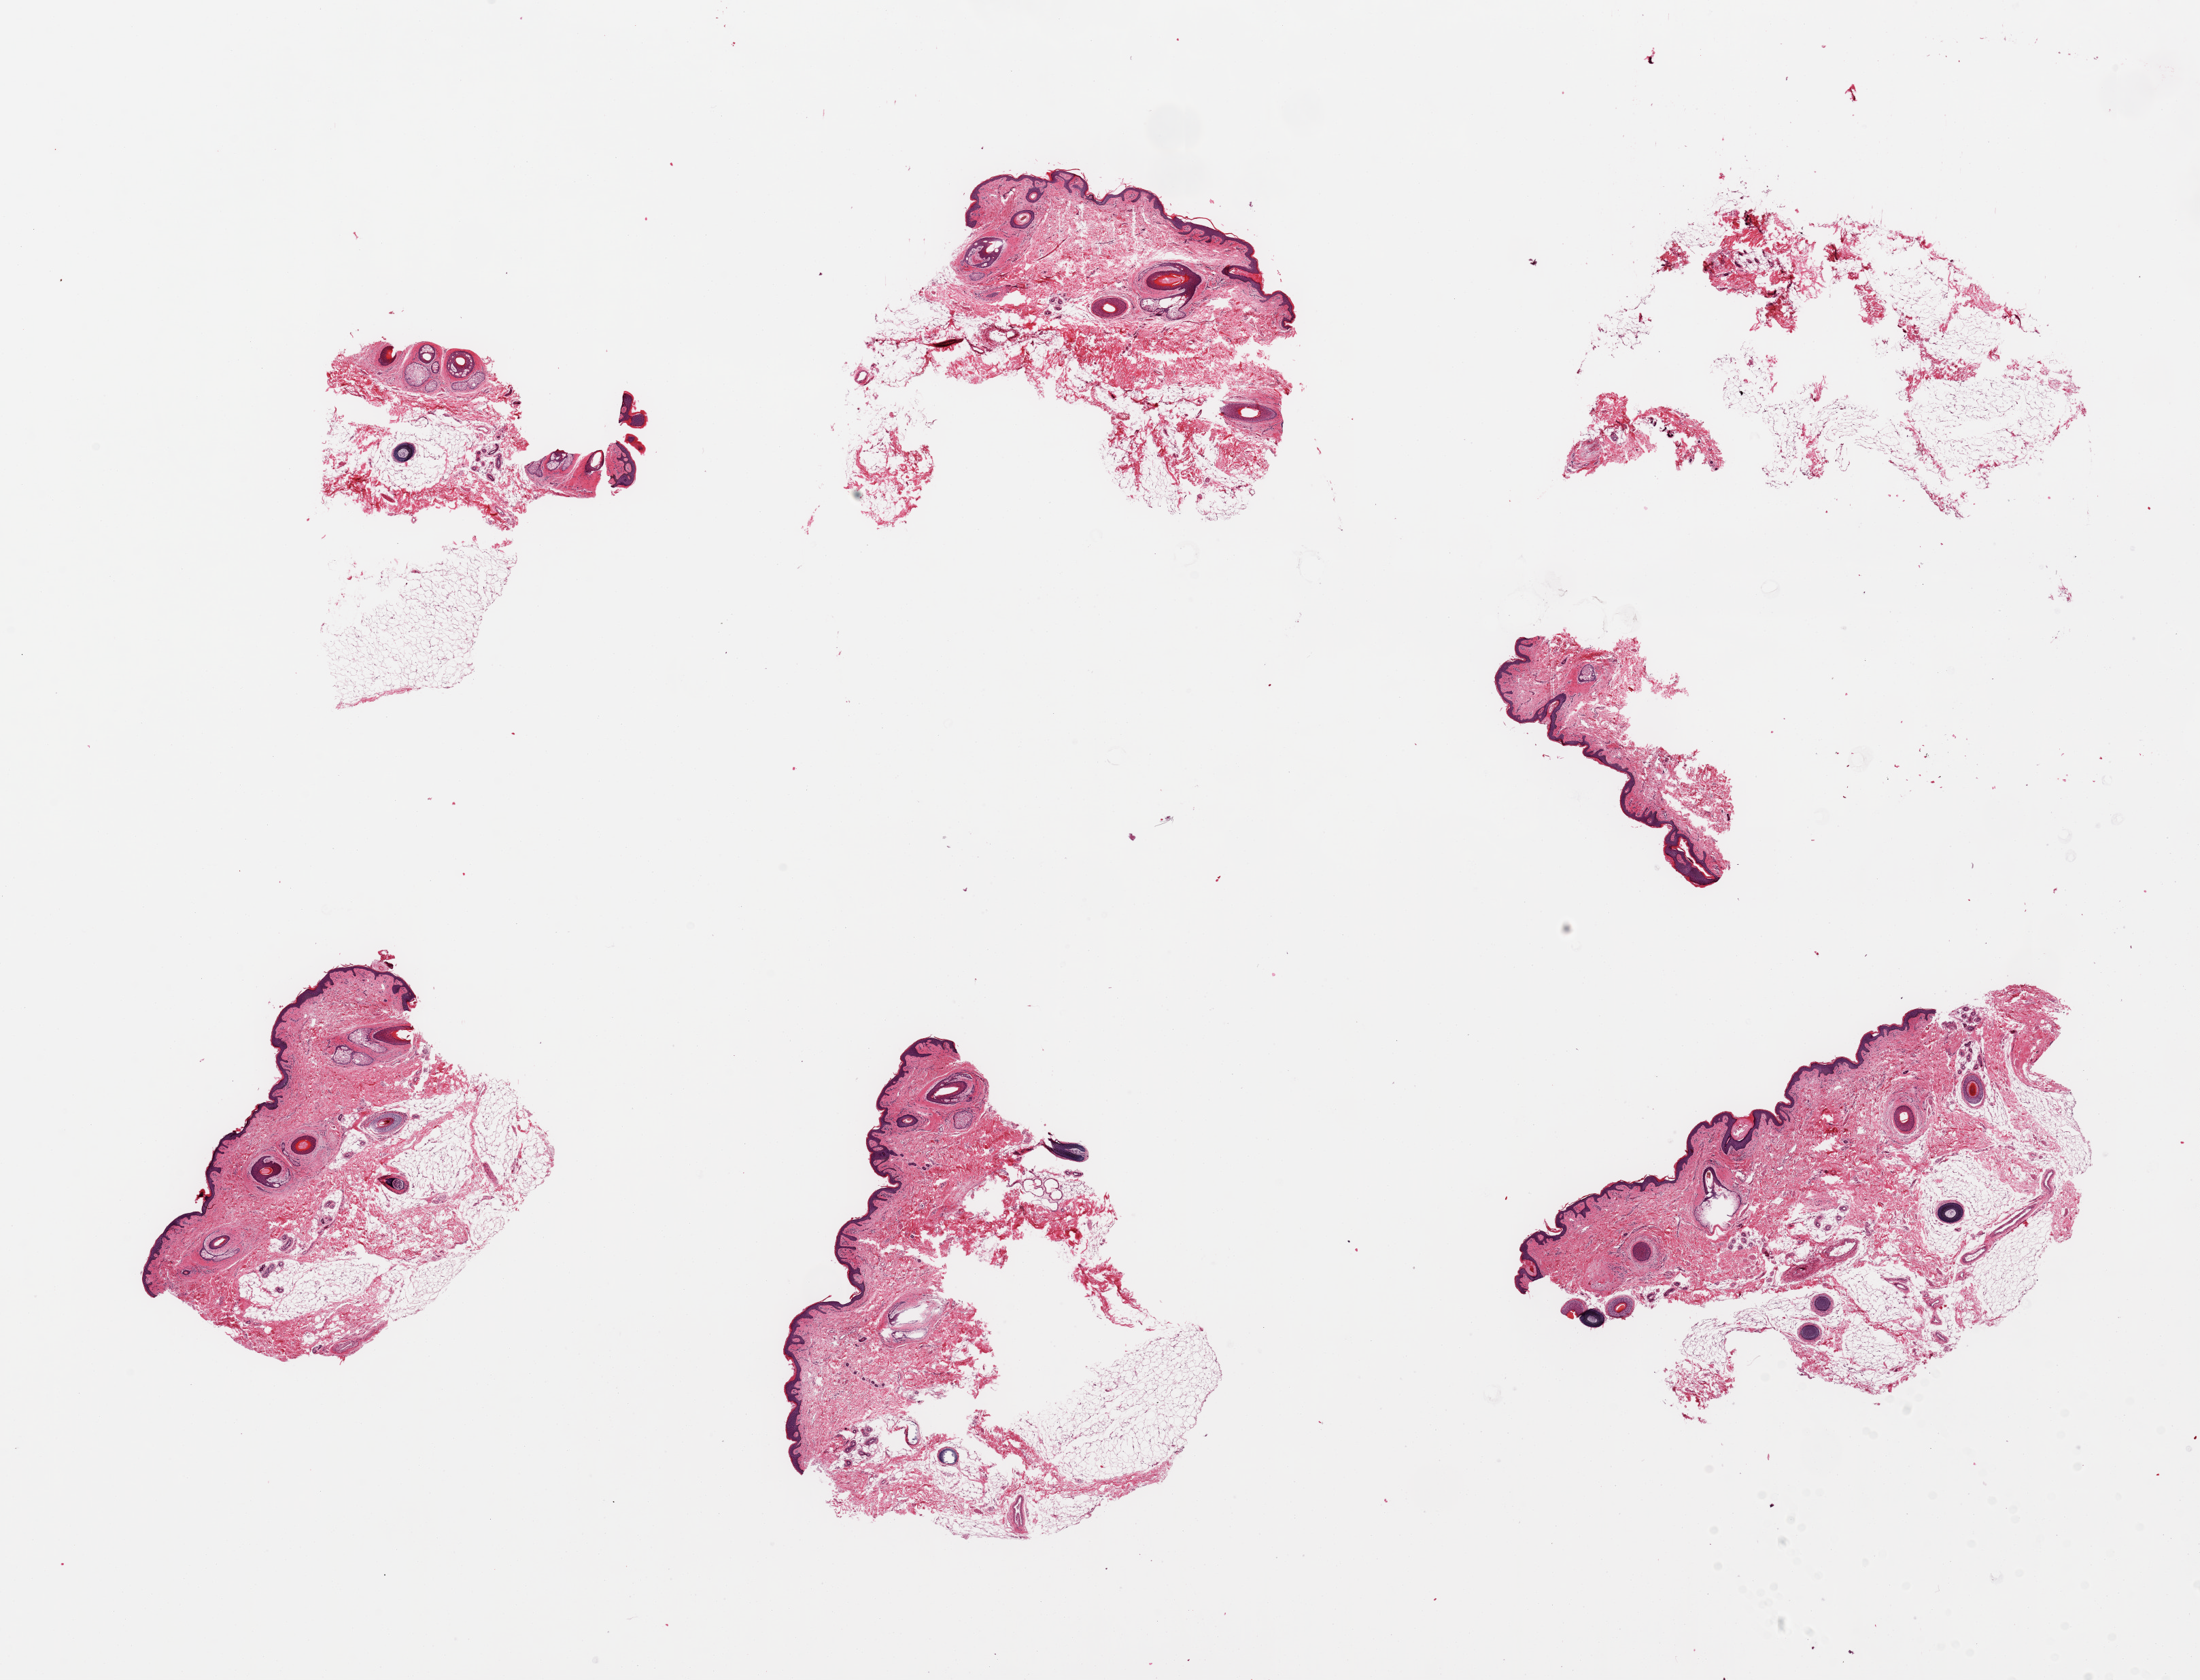
Whole-slide image, H&E stain — a low-resolution overview of the entire scanned area, about 25.6 x 19.5 mm (from a 20x scan), PAXgene-fixed paraffin-embedded (PFPE) section, sampled site (target tissue): skin of suprapubic region, tissue donor sample. Donor: male.
• review note (as recorded): 6 pieces with some fragmention; hair bearing skin with up to ~50% external fat; numerous hair follicles